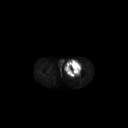
FDG PET of an extremity soft-tissue mass (from a PET/CT study), one axial slice. Slice 248 of 267 in the series (ordered by position). 128 × 128 image matrix, field of view 700 × 700 mm. Patient: male, 63 years. Case-level facts recorded for this patient, not image findings: histological type: pleiomorphic liposarcoma; grade: high; site of the primary tumour: left thigh.
Outlined on this slice (expert contour drawn on MRI and transferred to this co-registered scan by the dataset authors):
- gross tumour volume including surrounding oedema: bounding box <65,60,82,75> (left, top, right, bottom; pixels)
- gross tumour volume (mass): <65,60,81,75>